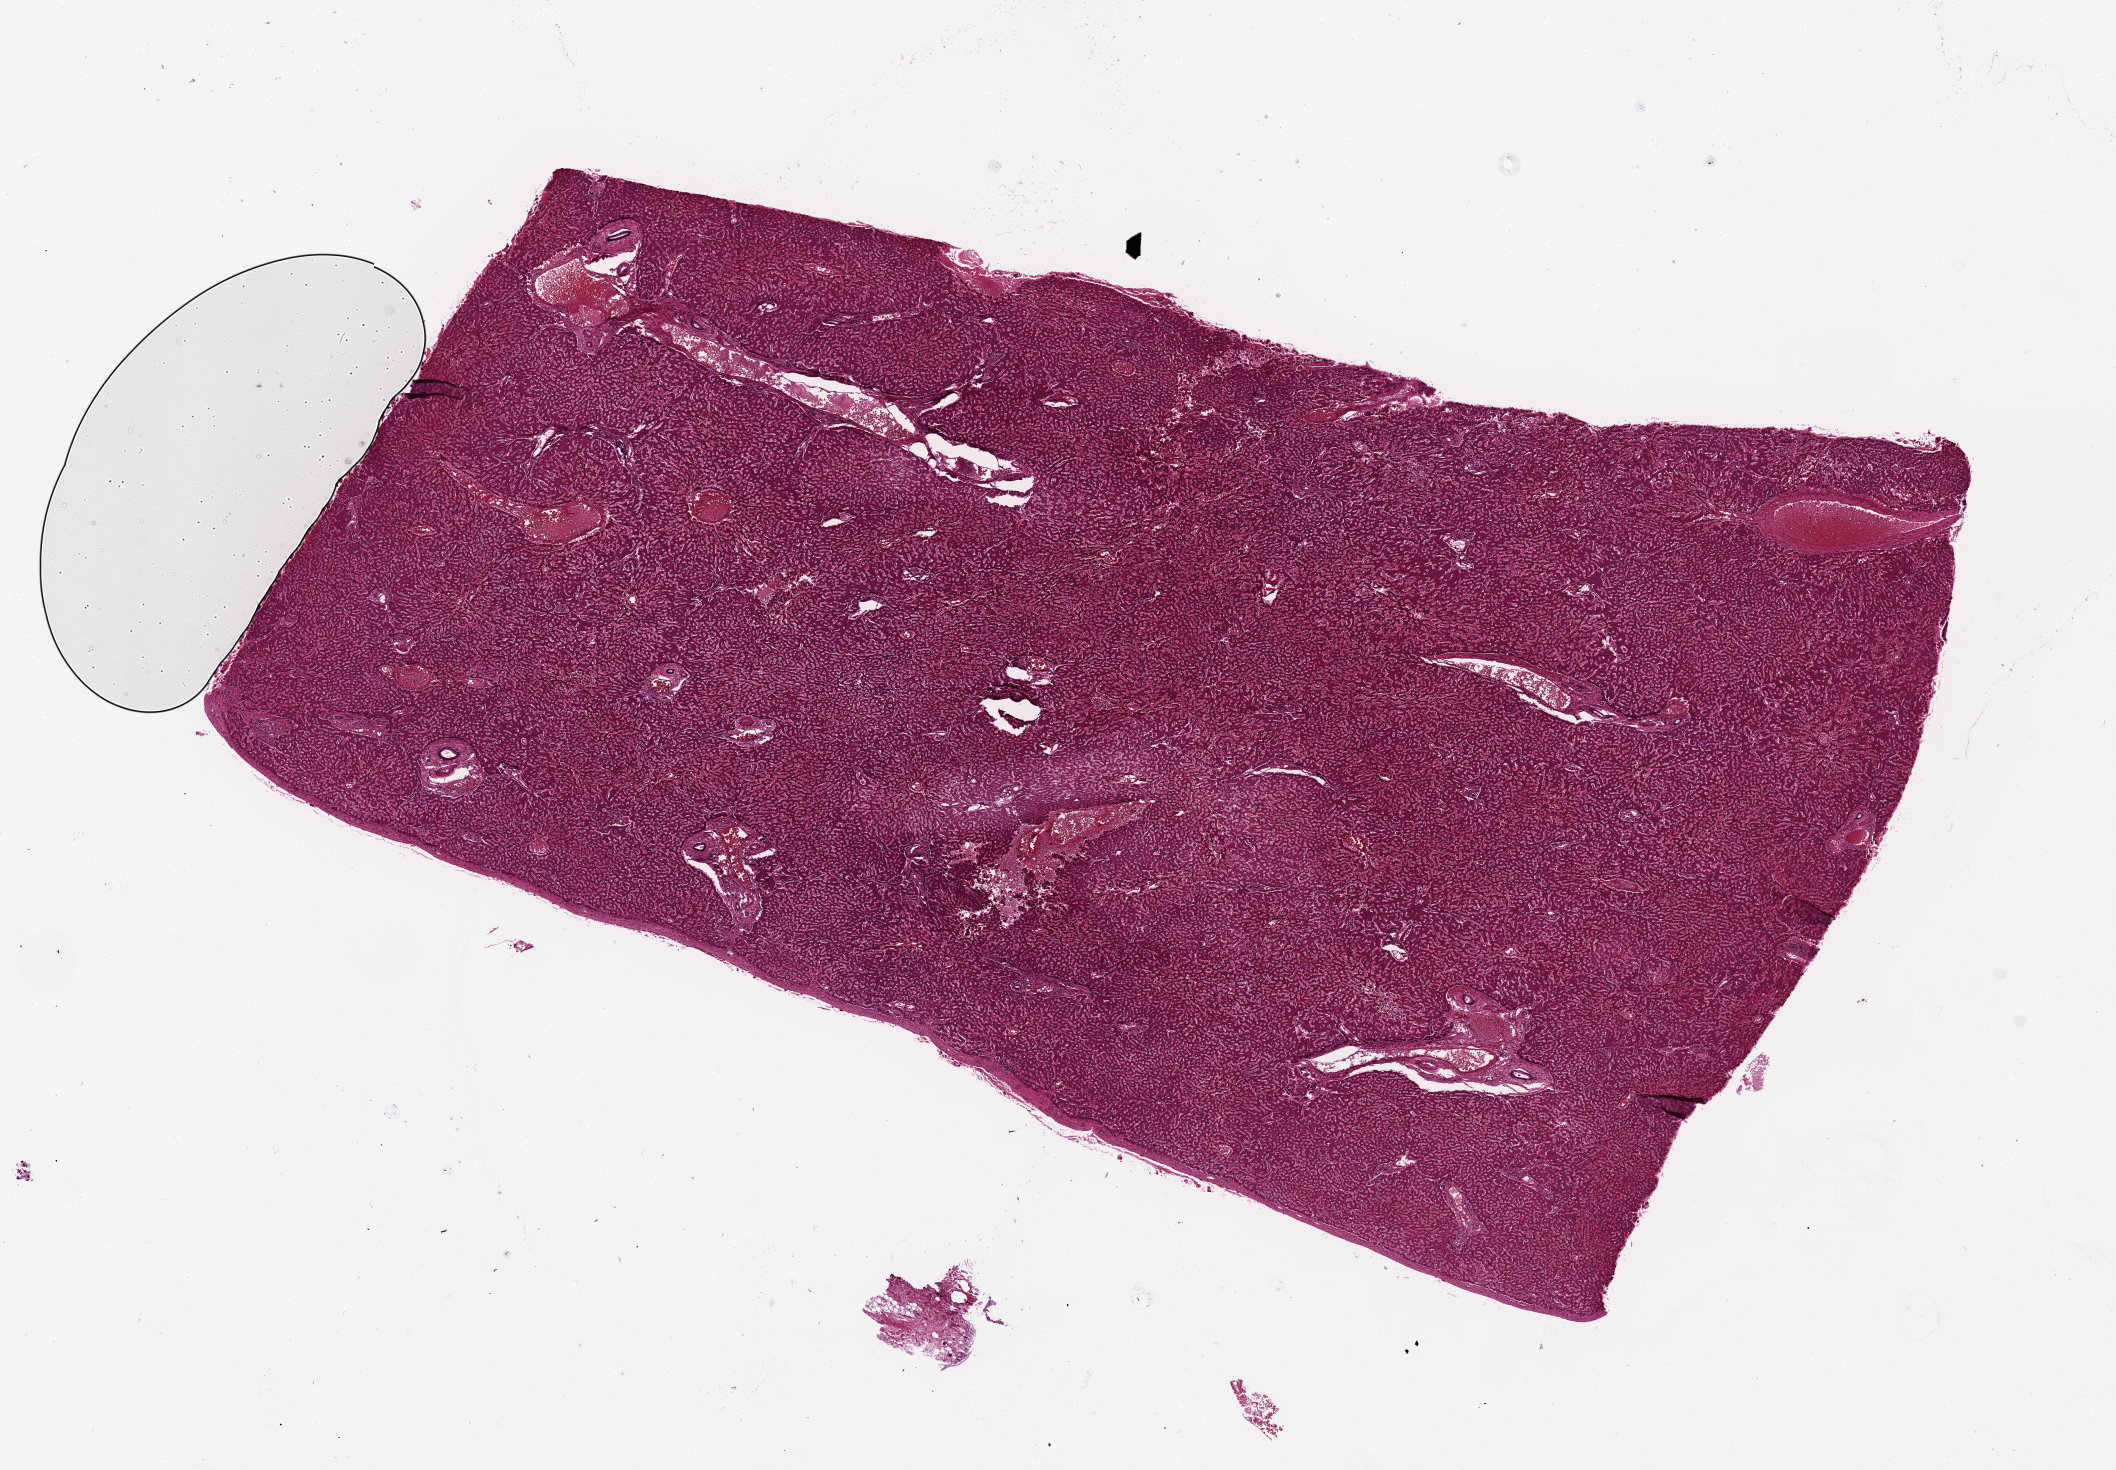
Haematoxylin and eosin whole-slide image, whole scanned area (about 16.7 x 11.6 mm) shown as a low-resolution overview. PAXgene-fixed paraffin-embedded (PFPE) section. Target tissue: liver. Tissue donor sample.
* pathologist's review note for this sample: 12x7 mm; apsule present; should be 1 cm deeper